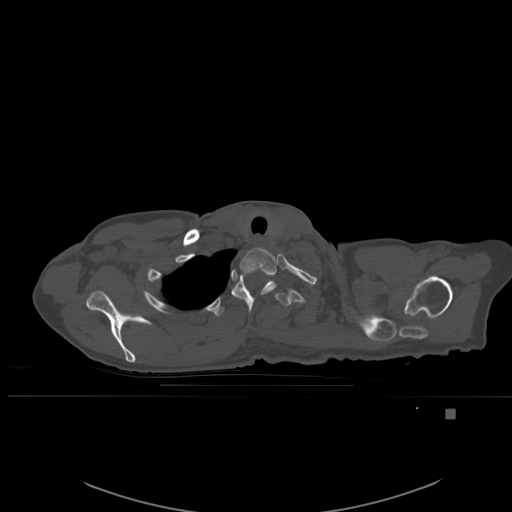
CT including the spine, one axial slice. Position 440 of 537 along the scan axis. Bone window (W 1800 / L 400 HU). 1.5 mm slice thickness. 512 × 512 image matrix, field of view 440 × 440 mm. Female patient, age 45 years. Case-level facts recorded for this patient, not image findings: primary cancer: lung.
Outlined on this slice (semi-automatic segmentation, software-assisted and operator-edited):
- T1 vertebra: bounding box <239,248,277,280> (left, top, right, bottom; pixels)
- T2 vertebra: <231,279,290,314>
- T3 vertebra: <213,304,225,317>